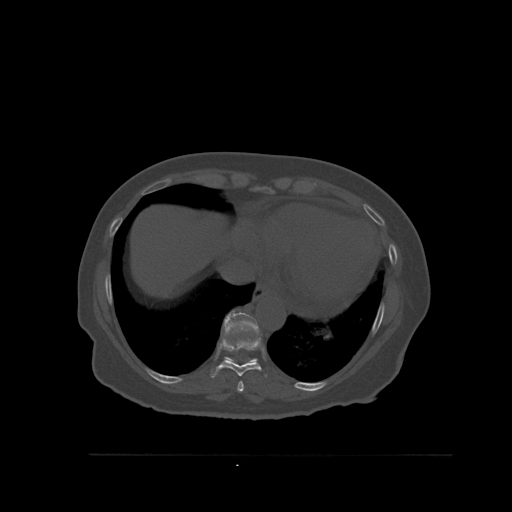
CT including the spine, one axial slice; position 332 of 527 along the scan axis; bone window (W 1800 / L 400 HU); 512 × 512 image matrix, field of view 470 × 470 mm. Patient: female, 73 years. Case-level facts recorded for this patient, not image findings: primary cancer: breast; vertebrae with lytic lesions (as recorded): L2.
Outlined on this slice (semi-automatically segmented with operator editing):
- T10 vertebra: box from (x=223, y=311) to (x=260, y=363) px
- T8 vertebra: (x=237, y=381)–(x=244, y=392)
- T9 vertebra: (x=210, y=334)–(x=267, y=378)